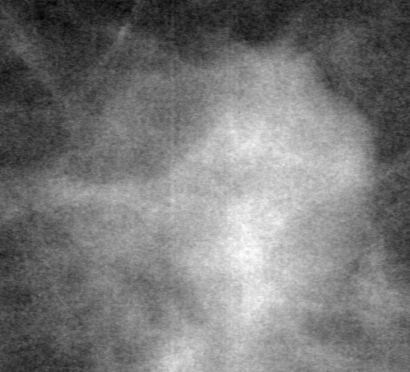
Crop from a digitized film mammogram around one marked abnormality, left breast, CC view, BI-RADS breast density category 2 (scale 1–4).
Mass, shape oval, margins obscured; BI-RADS assessment category 0; subtlety rating 5 on a 1 (subtle) to 5 (obvious) scale; pathology (as recorded): benign.